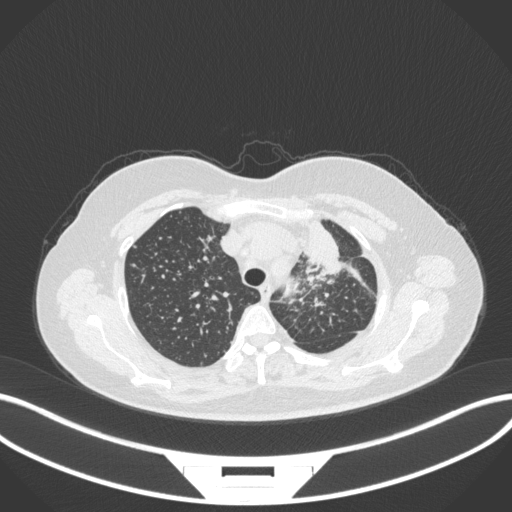
Chest CT, one axial slice. Position 263 of 348 along the scan axis. Reconstruction kernel B31f. 120 kVp. Lung window (W 1500 / L -600 HU). 512 × 512 image matrix. Female patient, age 49 years. From the clinical record (not read from this slice): clinical TNM (as recorded): T1c N0 M1.
Outlined on this slice (bounding box drawn by a radiologist):
- lung tumour (recorded histology: adenocarcinoma): bounding box (x1, y1, x2, y2) in pixels: (302, 218, 348, 282)